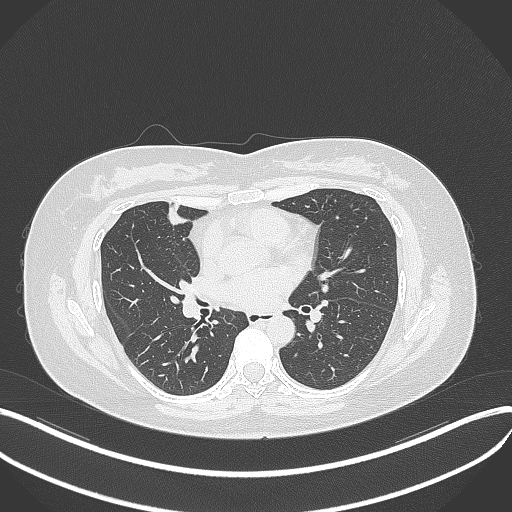
Chest CT, one axial slice. Position 160 of 273 along the scan axis. Lung window (W 1500 / L -600 HU). 1 mm slice thickness. 512 × 512 image matrix. Patient: female, 42 years. From the clinical record (not read from this slice): clinical TNM (as recorded): T1b N0 M0.
Annotated regions visible in this slice (bounding box drawn by a radiologist):
- lung tumour (recorded histology: adenocarcinoma): bounding box (x1, y1, x2, y2) in pixels: (163, 200, 188, 230)